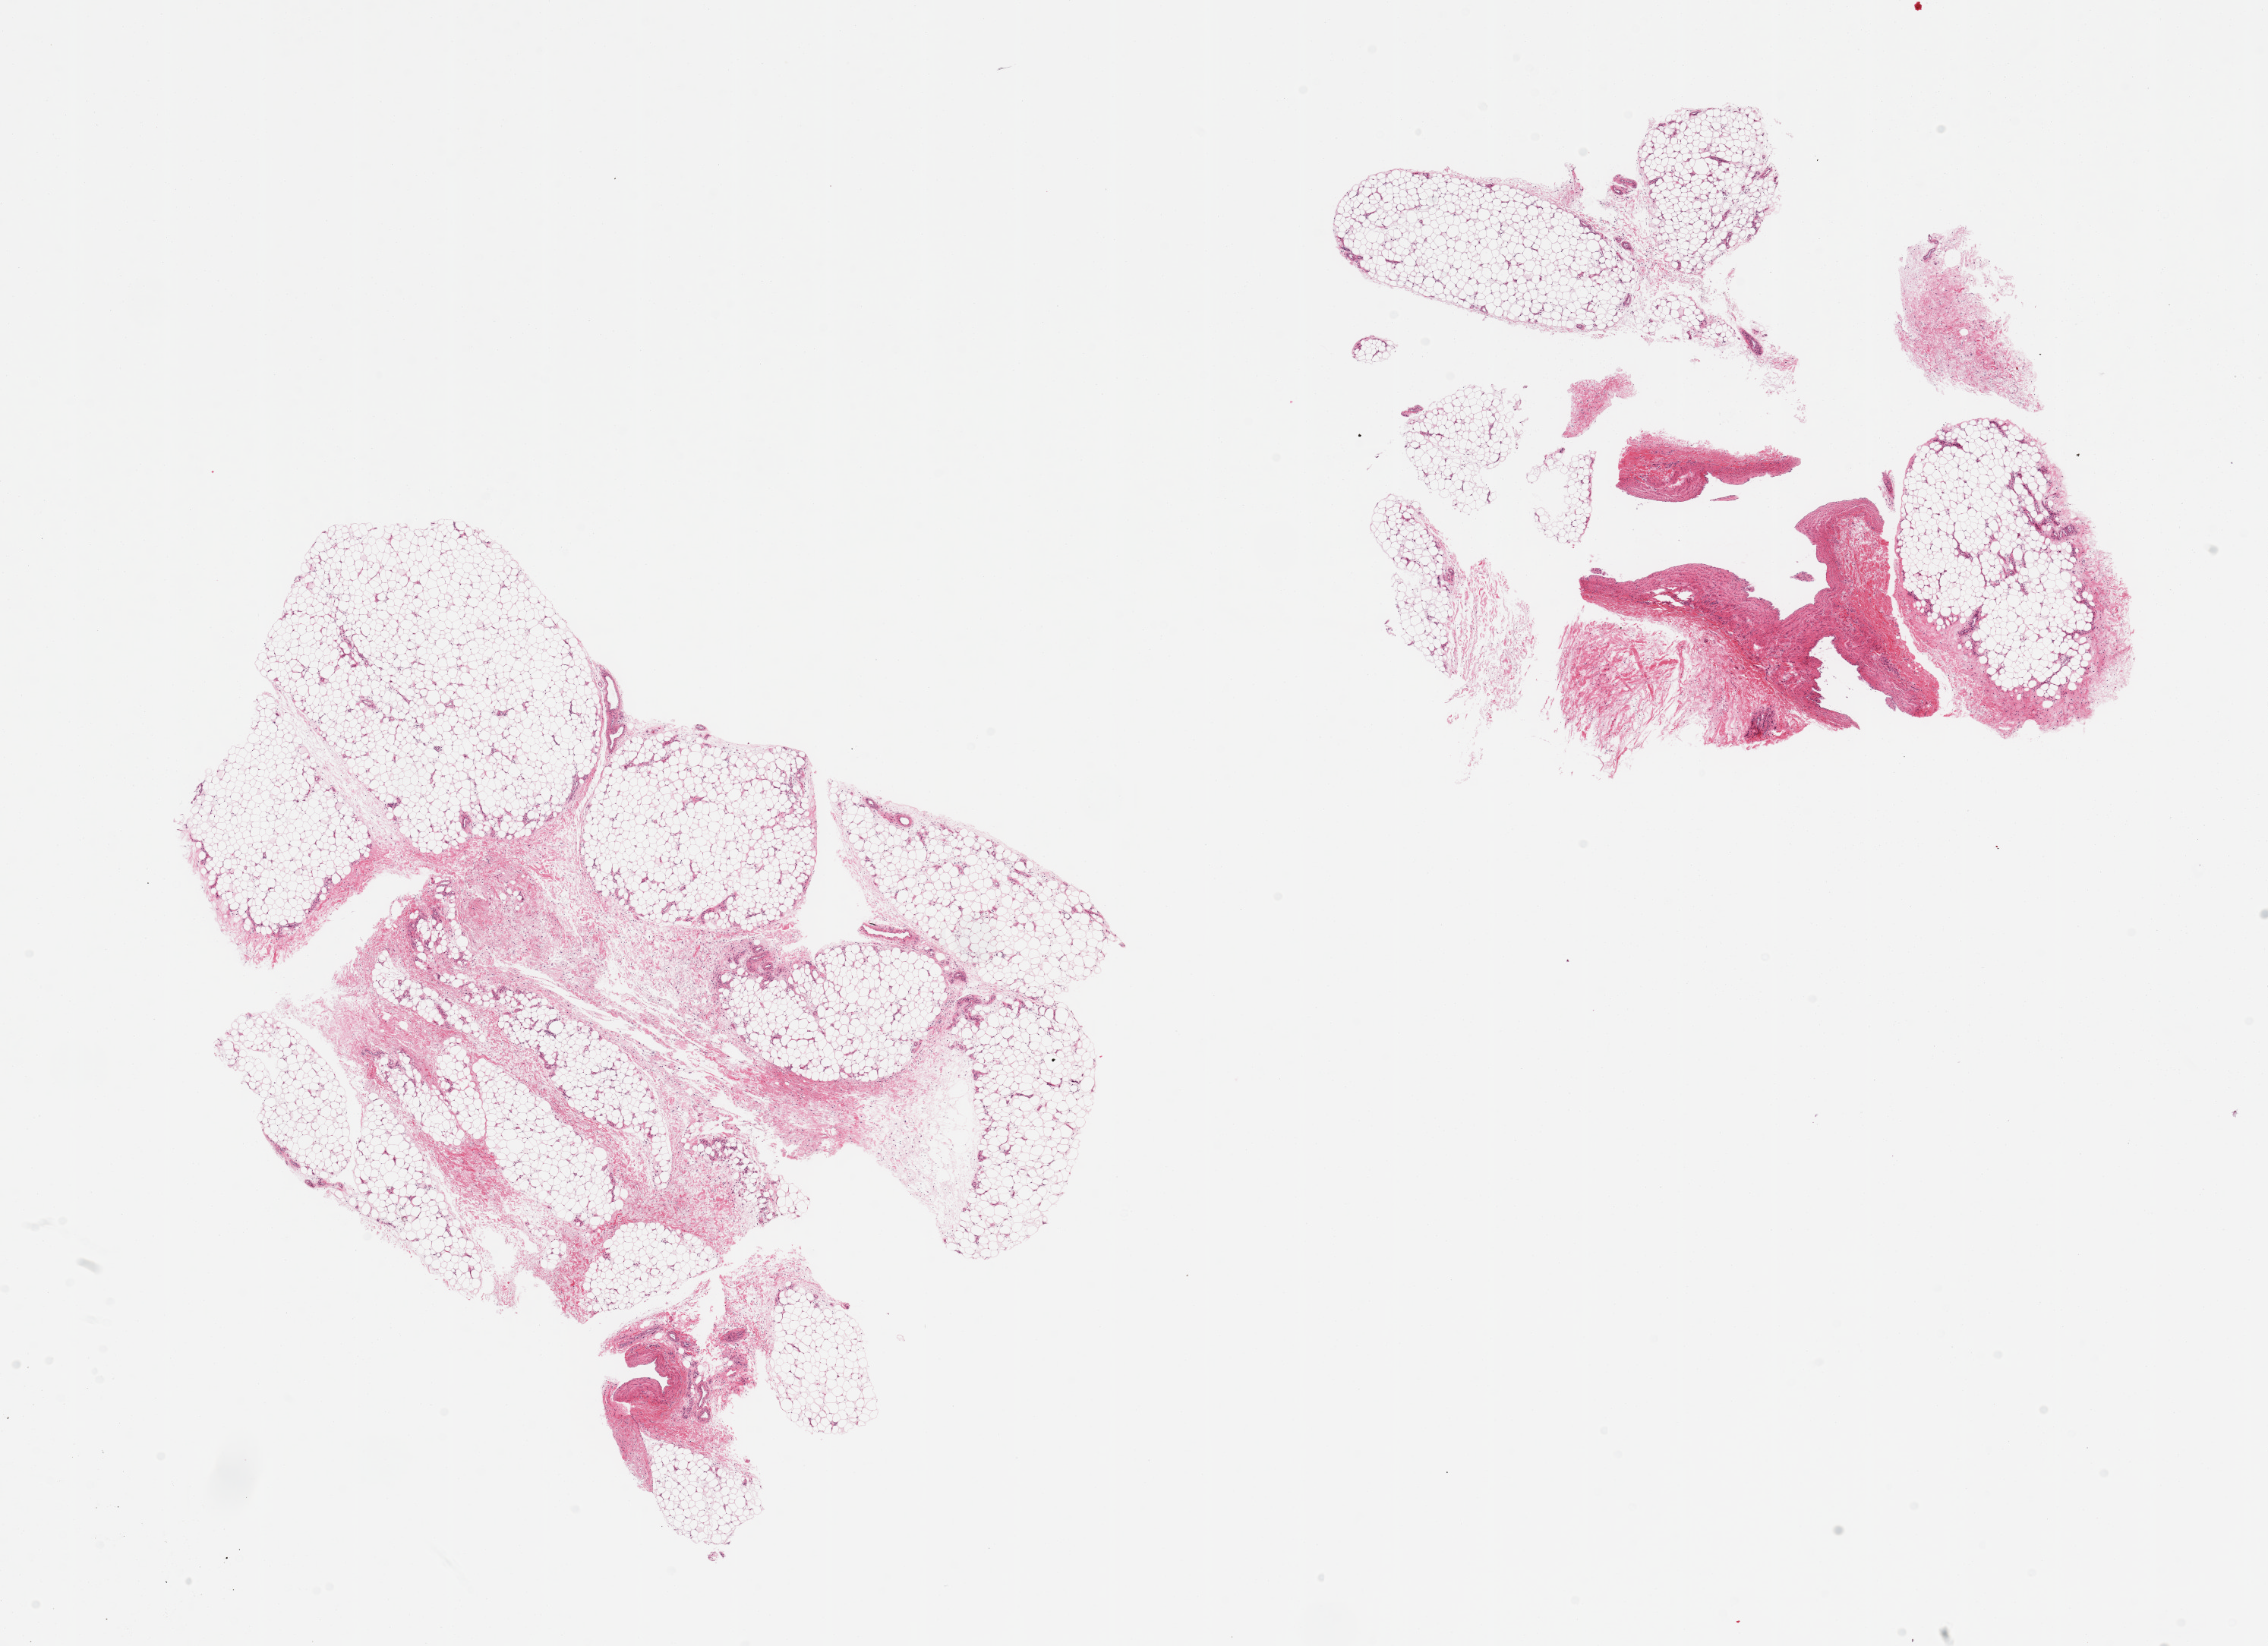
Digitized haematoxylin and eosin-stained section, brightfield, low-resolution overview of the scanned area, about 23.6 x 17.1 mm; PAXgene-fixed paraffin-embedded (PFPE) section; target tissue: adipose tissue; donor tissue sample. Donor: male.
• pathologist's review note for this sample: 2 pieces; 5% stromal content; portion of large blood vessel occupies 20%